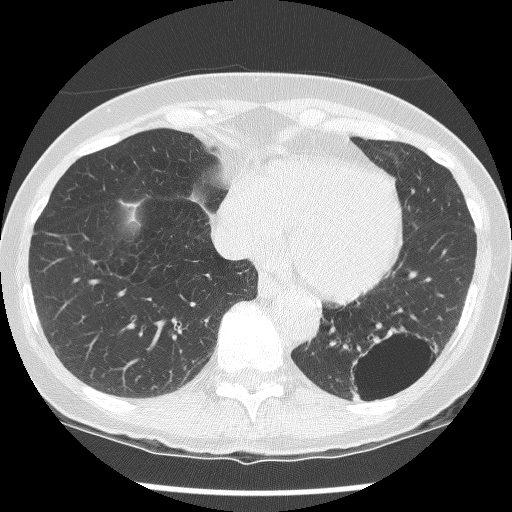
Low-dose screening chest CT, axial slice, second screening round (one year after baseline), lung window (W 1500 / L -600 HU), 2.5 mm slice thickness, slice 94 of 136 in the series, 512 × 512 image matrix. Female, age 61 years at enrolment.
Expert-annotated lung lesion, bounding box <331,322,438,415> (left, top, right, bottom; pixels). The screening reader recorded 2 non-calcified nodules or masses ≥4 mm on this exam (left lower lobe, left lower lobe); which of them this box marks is not recorded. Later outcome: lung cancer diagnosed 585 days after this screen (after the third annual screen) — non-small cell carcinoma, left lower lobe, poorly differentiated (G3), stage IB (AJCC 6th edition), 100 mm at pathology.